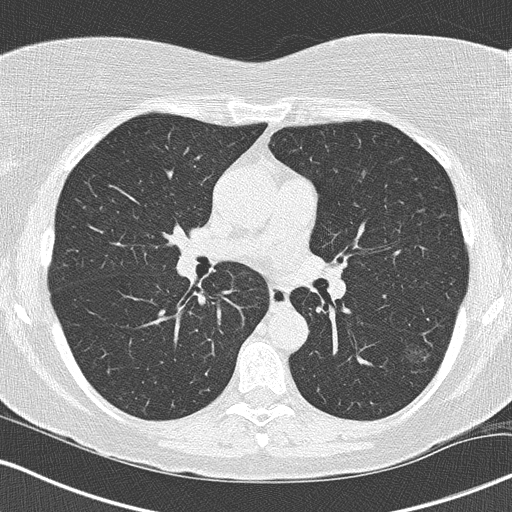
Low-dose screening chest CT, one axial slice. Position 84 of 160 along the scan axis. Reconstruction kernel B50f. 120 kVp. Lung window (W 1500 / L -600 HU). 2 mm slice thickness. 512 × 512 image matrix, field of view 327 × 327 mm.
Annotated regions visible in this slice (expert manual segmentation):
- lesion 1 (tumor, lower lobe of left lung): bounding box [x1, y1, x2, y2] px = [405, 345, 430, 364]